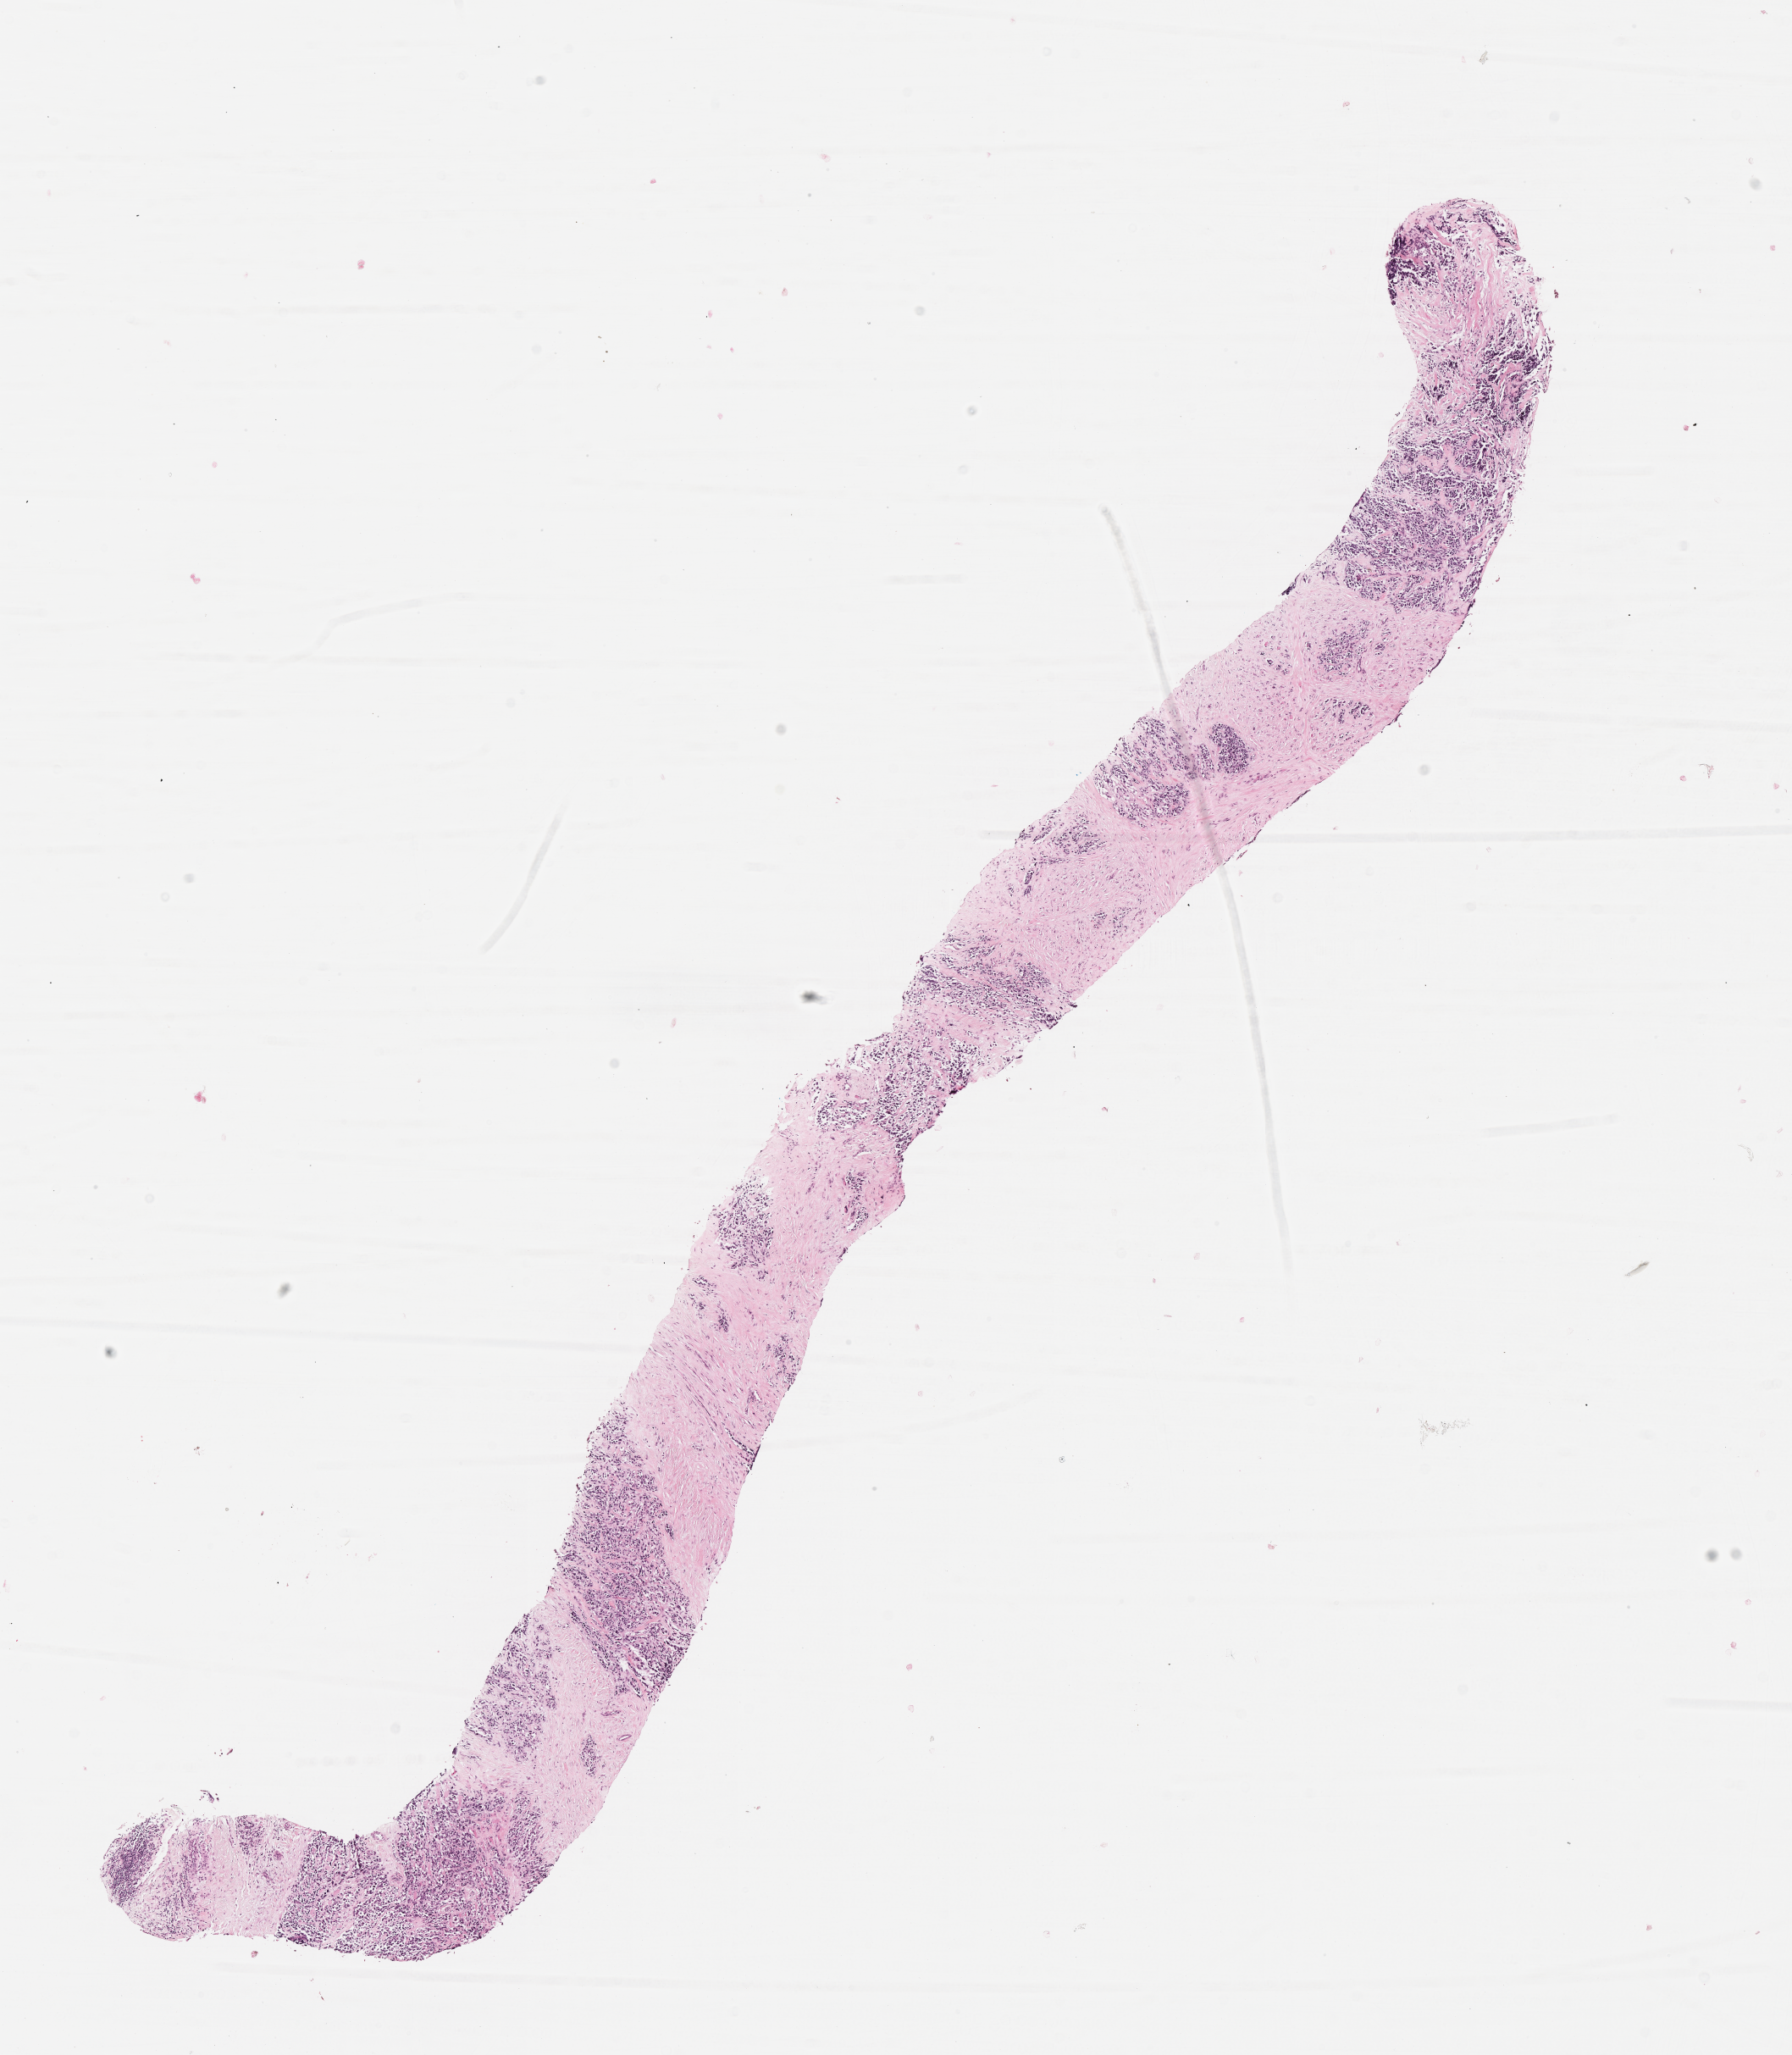
Hematoxylin and eosin (H&E) whole-slide image of tumor tissue, whole scanned area (about 8.6 x 9.8 mm) shown as a low-resolution overview. FFPE section. Sample anatomic site: soft tissue, foot-left. Female patient, age at diagnosis 10.8 years.
Diagnosis: rhabdomyosarcoma; histological classification: alveolar rhabdomyosarcoma.